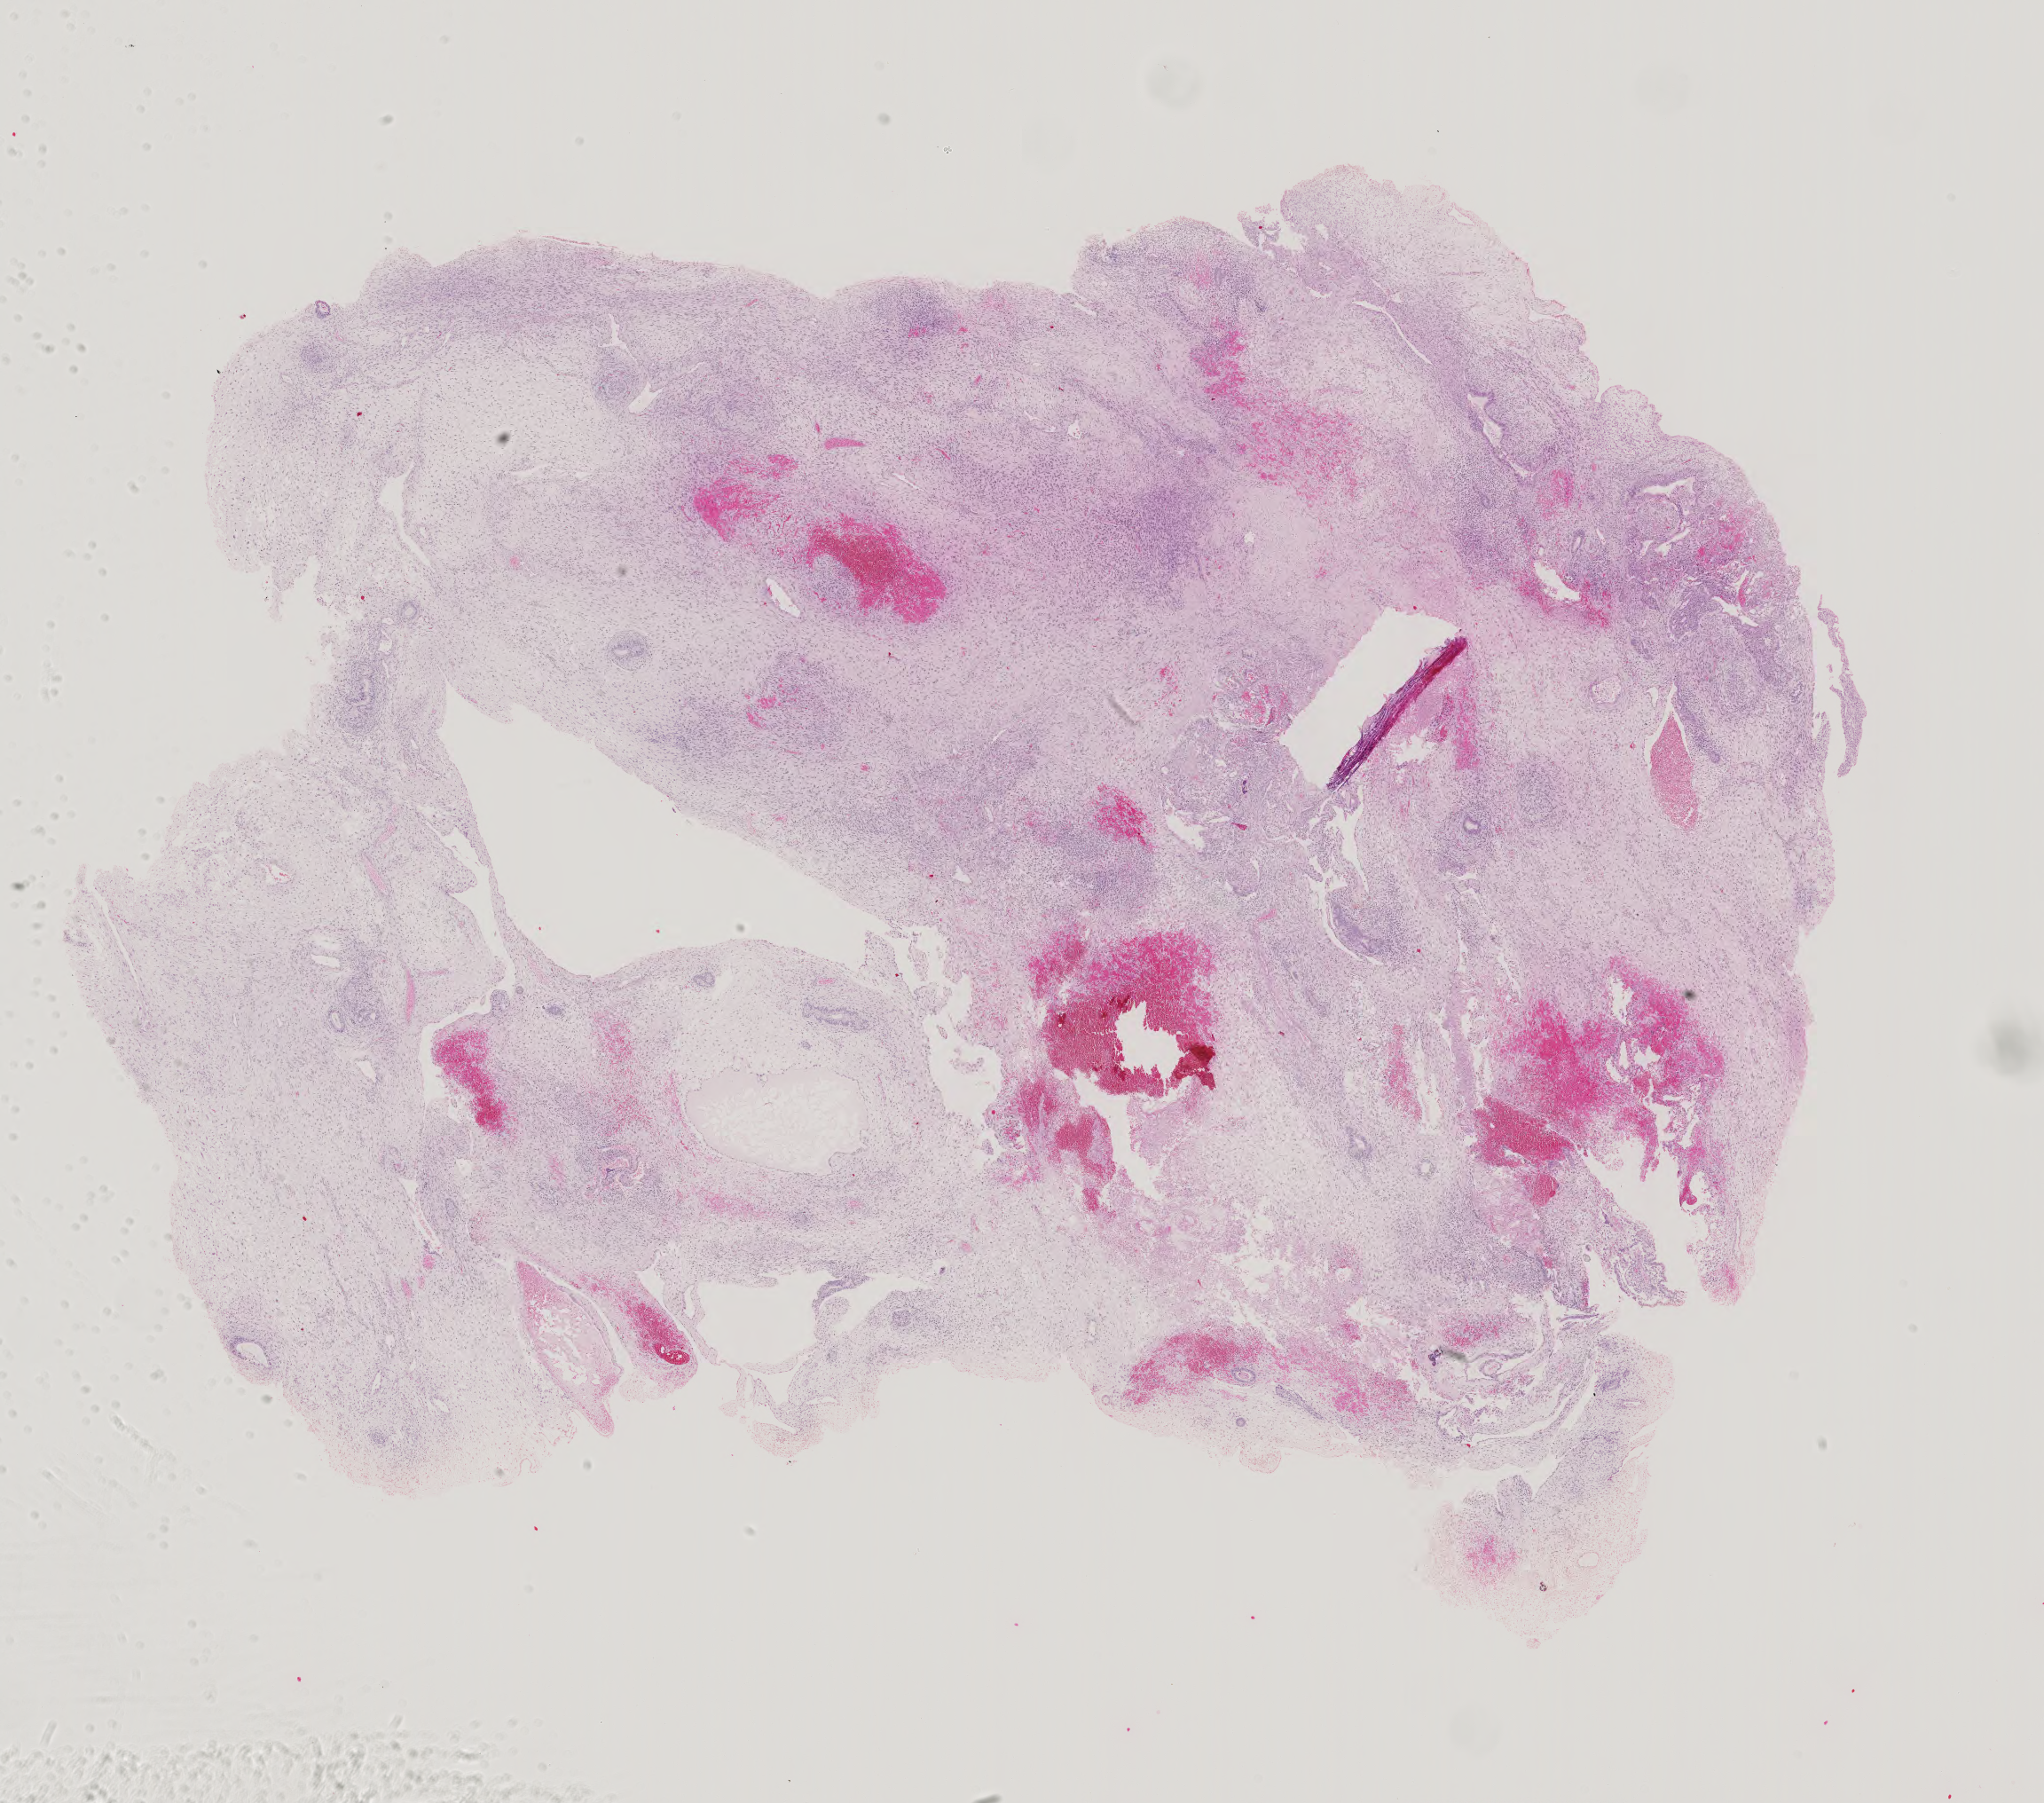
Digitized H&E-stained tissue section (whole slide), whole scanned area (about 16.8 x 14.8 mm) shown as a low-resolution overview. Male patient.
* specimen: formalin-fixed paraffin-embedded (FFPE) diagnostic section; primary tumour sample from the testis